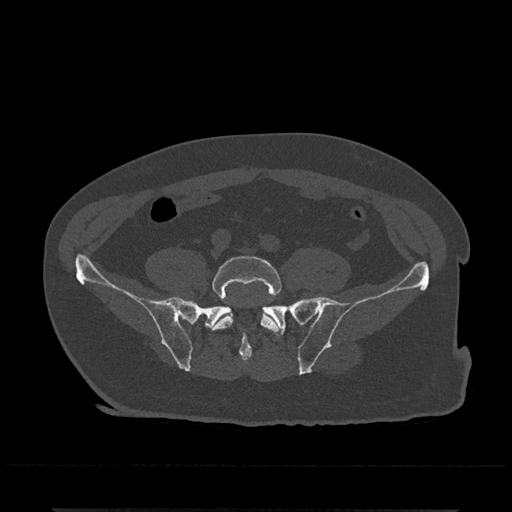
CT including the spine, one axial slice. Position 60 of 797 along the scan axis. Bone window (W 1800 / L 400 HU). 512 × 512 image matrix, field of view 393 × 393 mm. Patient: male, 67 years. From the clinical record (not read from this slice): primary cancer: prostate.
Structures marked on this image (semi-automatic segmentation, software-assisted and operator-edited):
- L5 vertebra: box from (x=210, y=255) to (x=282, y=332) px